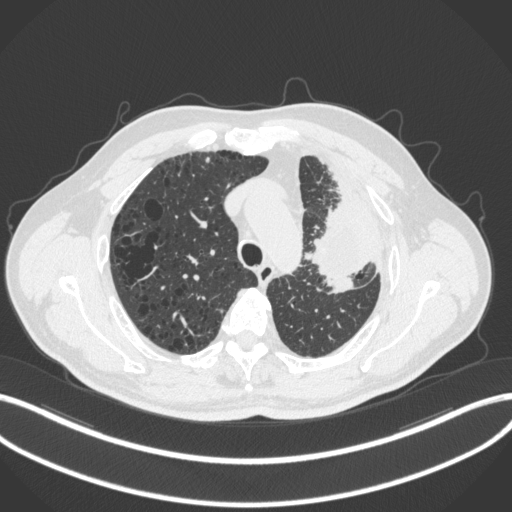
Chest CT, one axial slice. Position 230 of 286 along the scan axis. Lung window (W 1500 / L -600 HU). 512 × 512 image matrix, field of view 400 × 400 mm. Male patient, age 68 years. From the clinical record (not read from this slice): clinical TNM (as recorded): T3 N3 M1.
Outlined on this slice (rectangle marked by the reading radiologist):
- lung tumour (recorded histology: adenocarcinoma): bounding box [x1, y1, x2, y2] px = [304, 187, 380, 294]